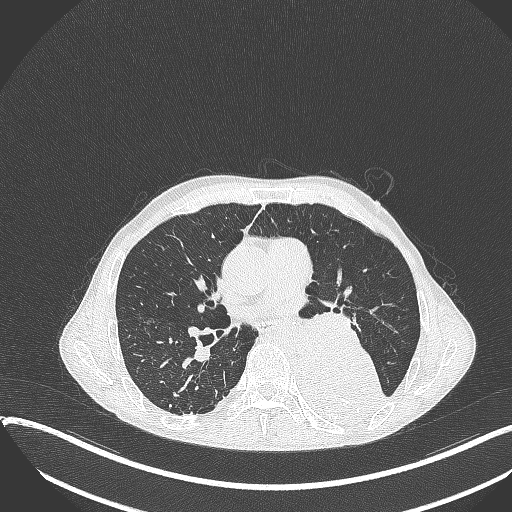
Chest CT, one axial slice; slice 197 of 401 in the series (ordered by position); 120 kVp; lung window (W 1500 / L -600 HU); 512 × 512 image matrix, field of view 400 × 400 mm. Male patient, age 57 years. Case-level facts recorded for this patient, not image findings: clinical TNM (as recorded): T4 N0 M0.
Annotated regions visible in this slice (rectangle marked by the reading radiologist):
- lung tumour (recorded histology: squamous cell carcinoma): bounding box (x1, y1, x2, y2) in pixels: (286, 329, 390, 422)